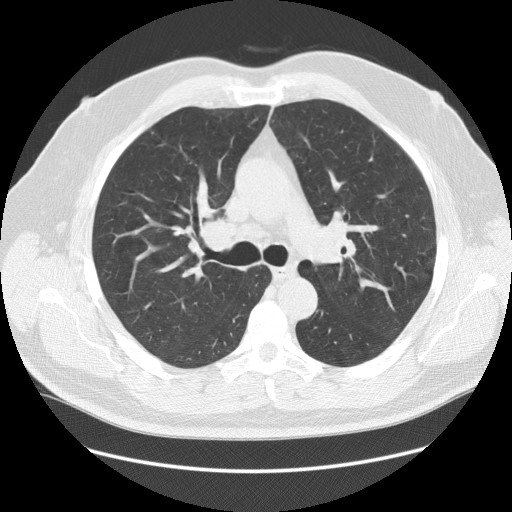
Chest CT (low-dose screening protocol), one axial image; baseline screening round; lung window (W 1500 / L -600 HU); 2.5 mm slice thickness; standard (soft-tissue) reconstruction kernel (STANDARD); slice 50 of 140 in the series. Male, age 64 years at enrolment. Former smoker at enrolment.
Lesion marked by an expert reader, bounding box (x1, y1, x2, y2) in pixels: (179, 205, 251, 272). Reader record for this screening exam (exam-level; its link to the box is not recorded): non-calcified nodule or mass ≥4 mm, right lower lobe, 7 × 5 mm, smooth margins, soft tissue attenuation. Official screen result: positive, change unspecified: nodule(s) >= 4 mm or enlarging nodule(s), mass(es), or other non-specific abnormalities suspicious for lung cancer. Later outcome: lung cancer diagnosed 456 days after this screen (after the second annual screen) — adenocarcinoma, NOS, right upper lobe, poorly differentiated (G3), stage IB (AJCC 6th edition), 37 mm at pathology.